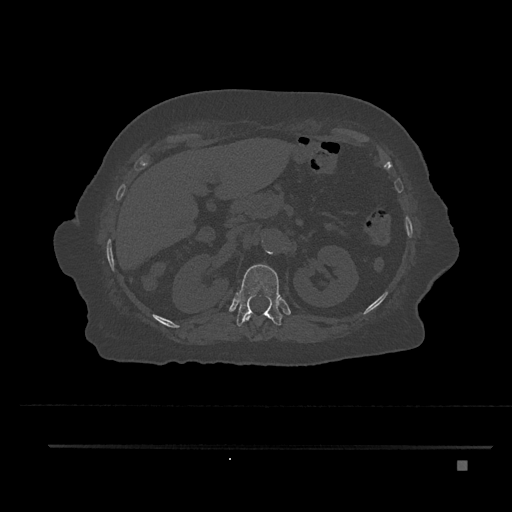
CT including the spine, one axial slice. Position 271 of 797 along the scan axis. Reconstruction kernel Br40s/3. 120 kVp. Bone window (W 1800 / L 400 HU). 0.5 mm slice thickness. 512 × 512 image matrix, field of view 437 × 437 mm. Patient: female, 76 years. From the clinical record (not read from this slice): primary cancer: lung.
Annotated regions visible in this slice (semi-automatically segmented with operator editing):
- T11 vertebra: box from (x=243, y=313) to (x=261, y=339) px
- T12 vertebra: (x=236, y=264)–(x=282, y=327)